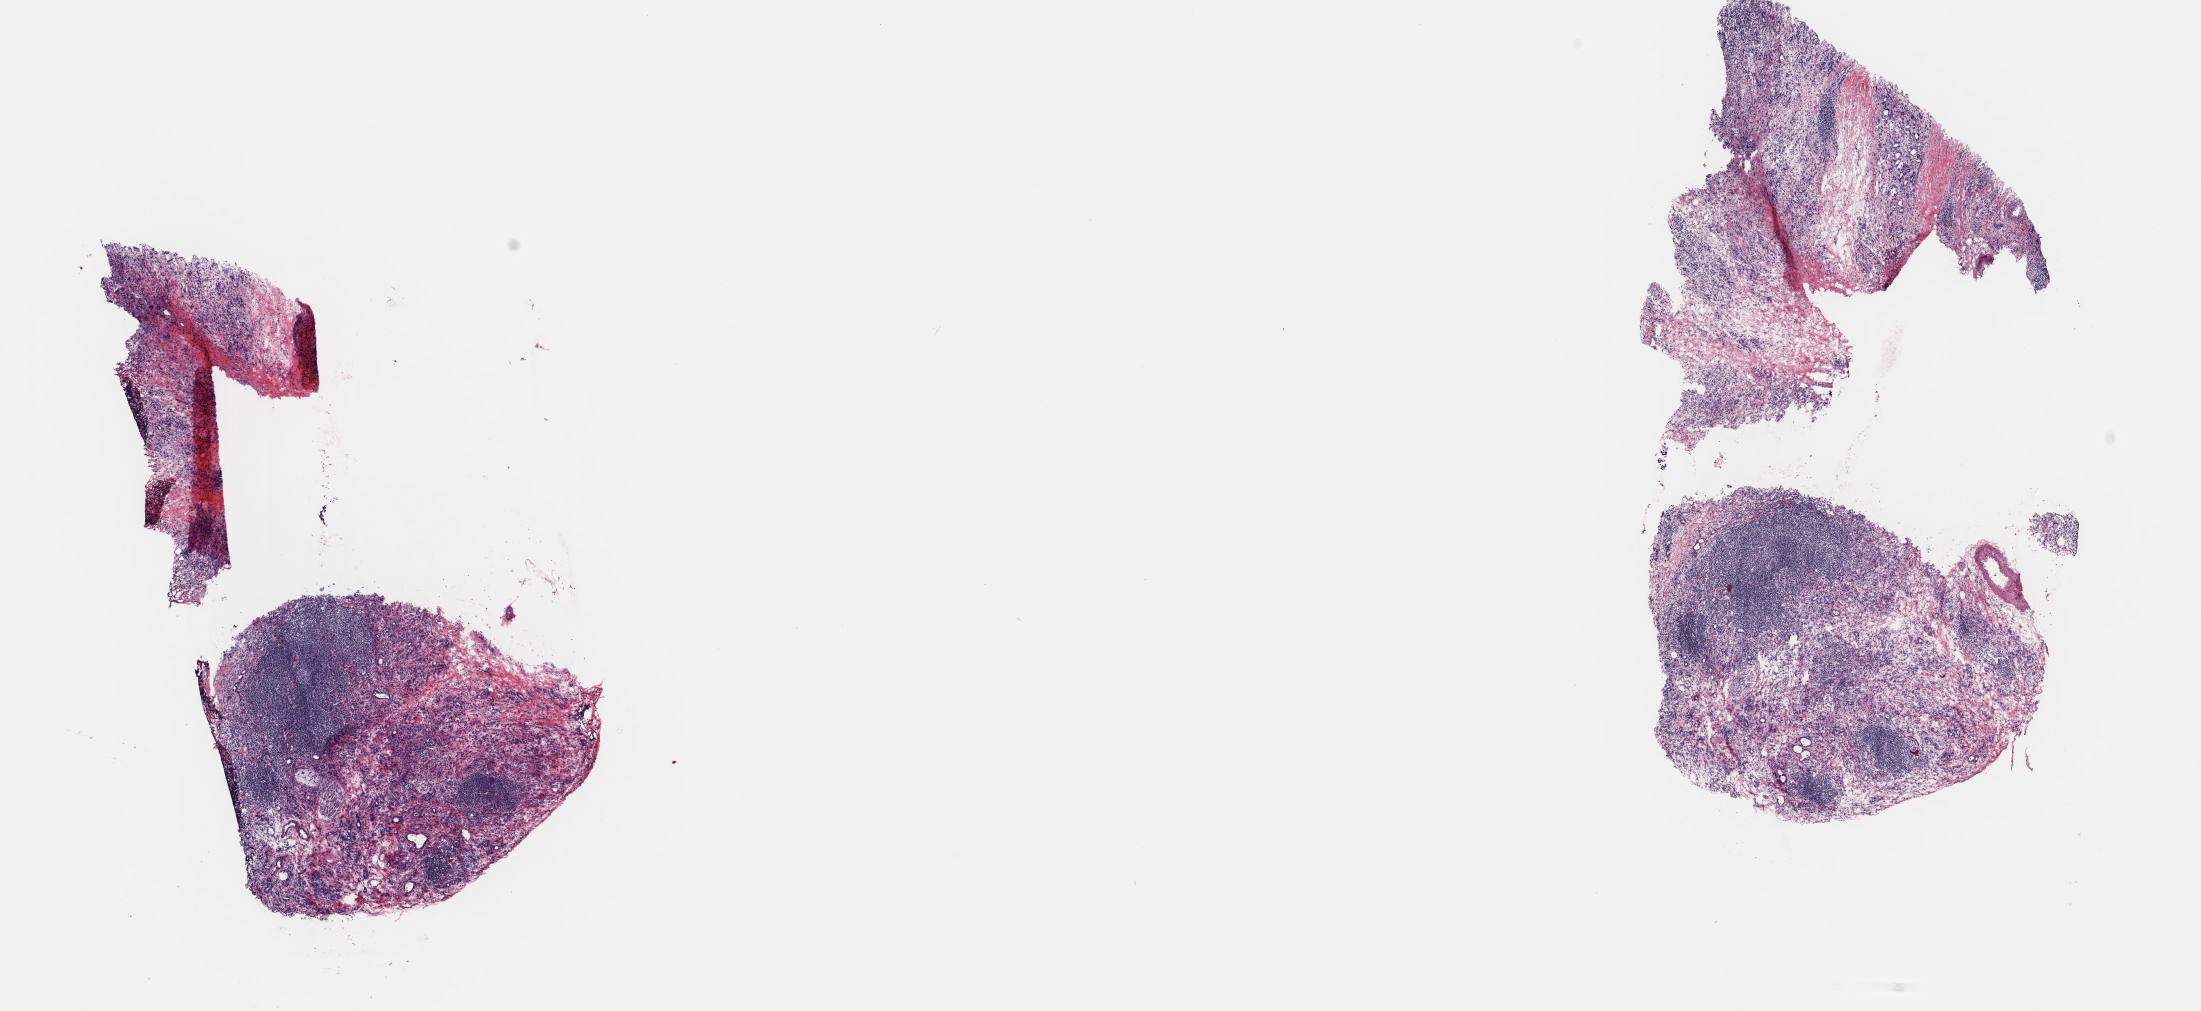
Whole-slide histology image, H&E-stained — shown as a low-resolution overview of the whole scanned area (about 17.4 x 8.0 mm, acquisition: 40x scan), frozen section from the top of the tissue portion, primary tumour sample from the stomach. Male patient; age at initial diagnosis 76 years. Histologic grade: G2 (moderately differentiated). Pathologist review of this section (percent, as recorded): tumour cells 100%, tumour nuclei 60%, normal cells 0%, stromal cells 0%, necrosis 0%. Infiltration values recorded for this section: lymphocyte infiltration 20%, monocyte infiltration 1%, neutrophil infiltration 1%.
- AJCC pathologic stage: IIIB
- histologic diagnosis: Tubular adenocarcinoma (fundus of stomach)
- lymph nodes positive (case pathology): 7 of 34 examined